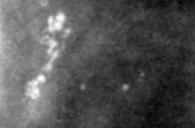
Cropped region of a digitized screen-film mammogram centred on a radiologist-marked abnormality, left breast, MLO view, BI-RADS breast density category 4 (scale 1–4).
Finding: calcifications, morphology pleomorphic, distribution clustered; BI-RADS assessment category 4; pathology (as recorded): malignant.